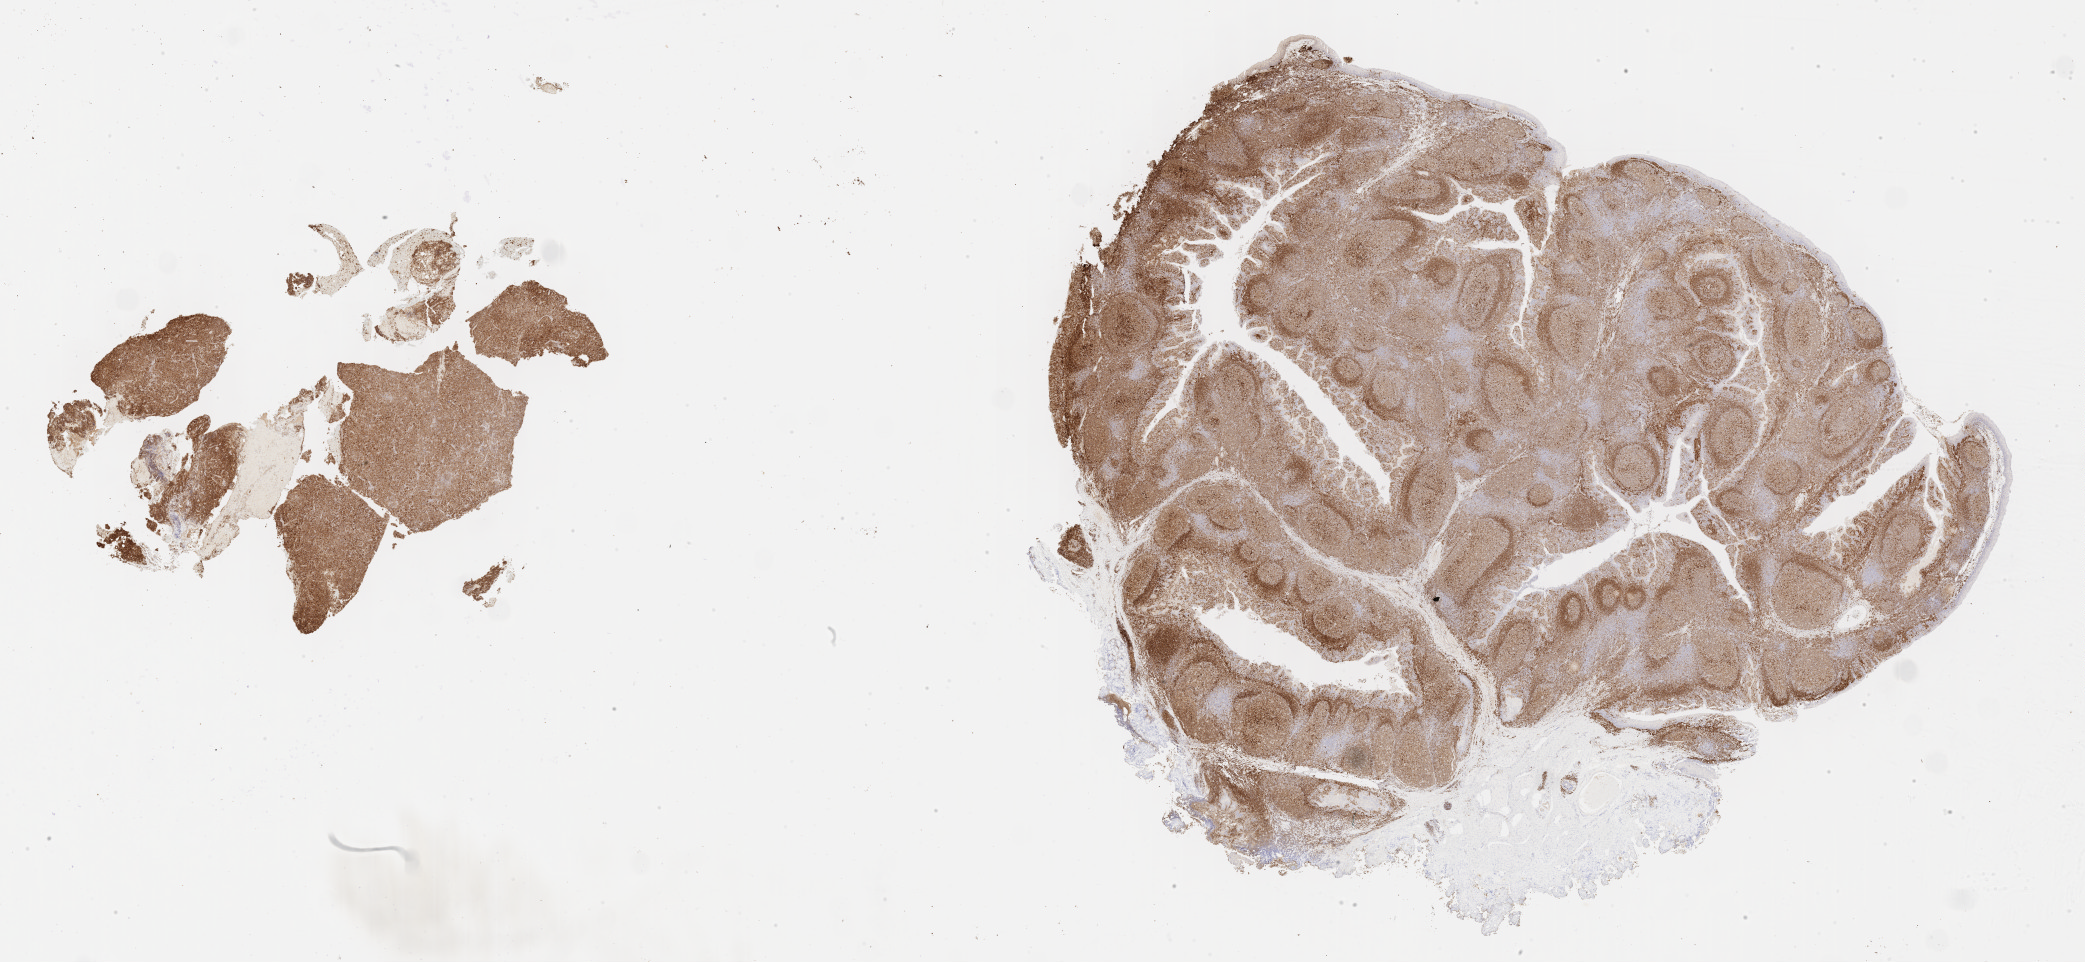
IHC for CD79a, whole-slide image — low-resolution overview of the scanned area, about 33.7 x 15.6 mm, specimen: tumor tissue, site: lymph node. Patient female; aged 71.
Histologic diagnosis: Diffuse large B-cell lymphoma, NOS.